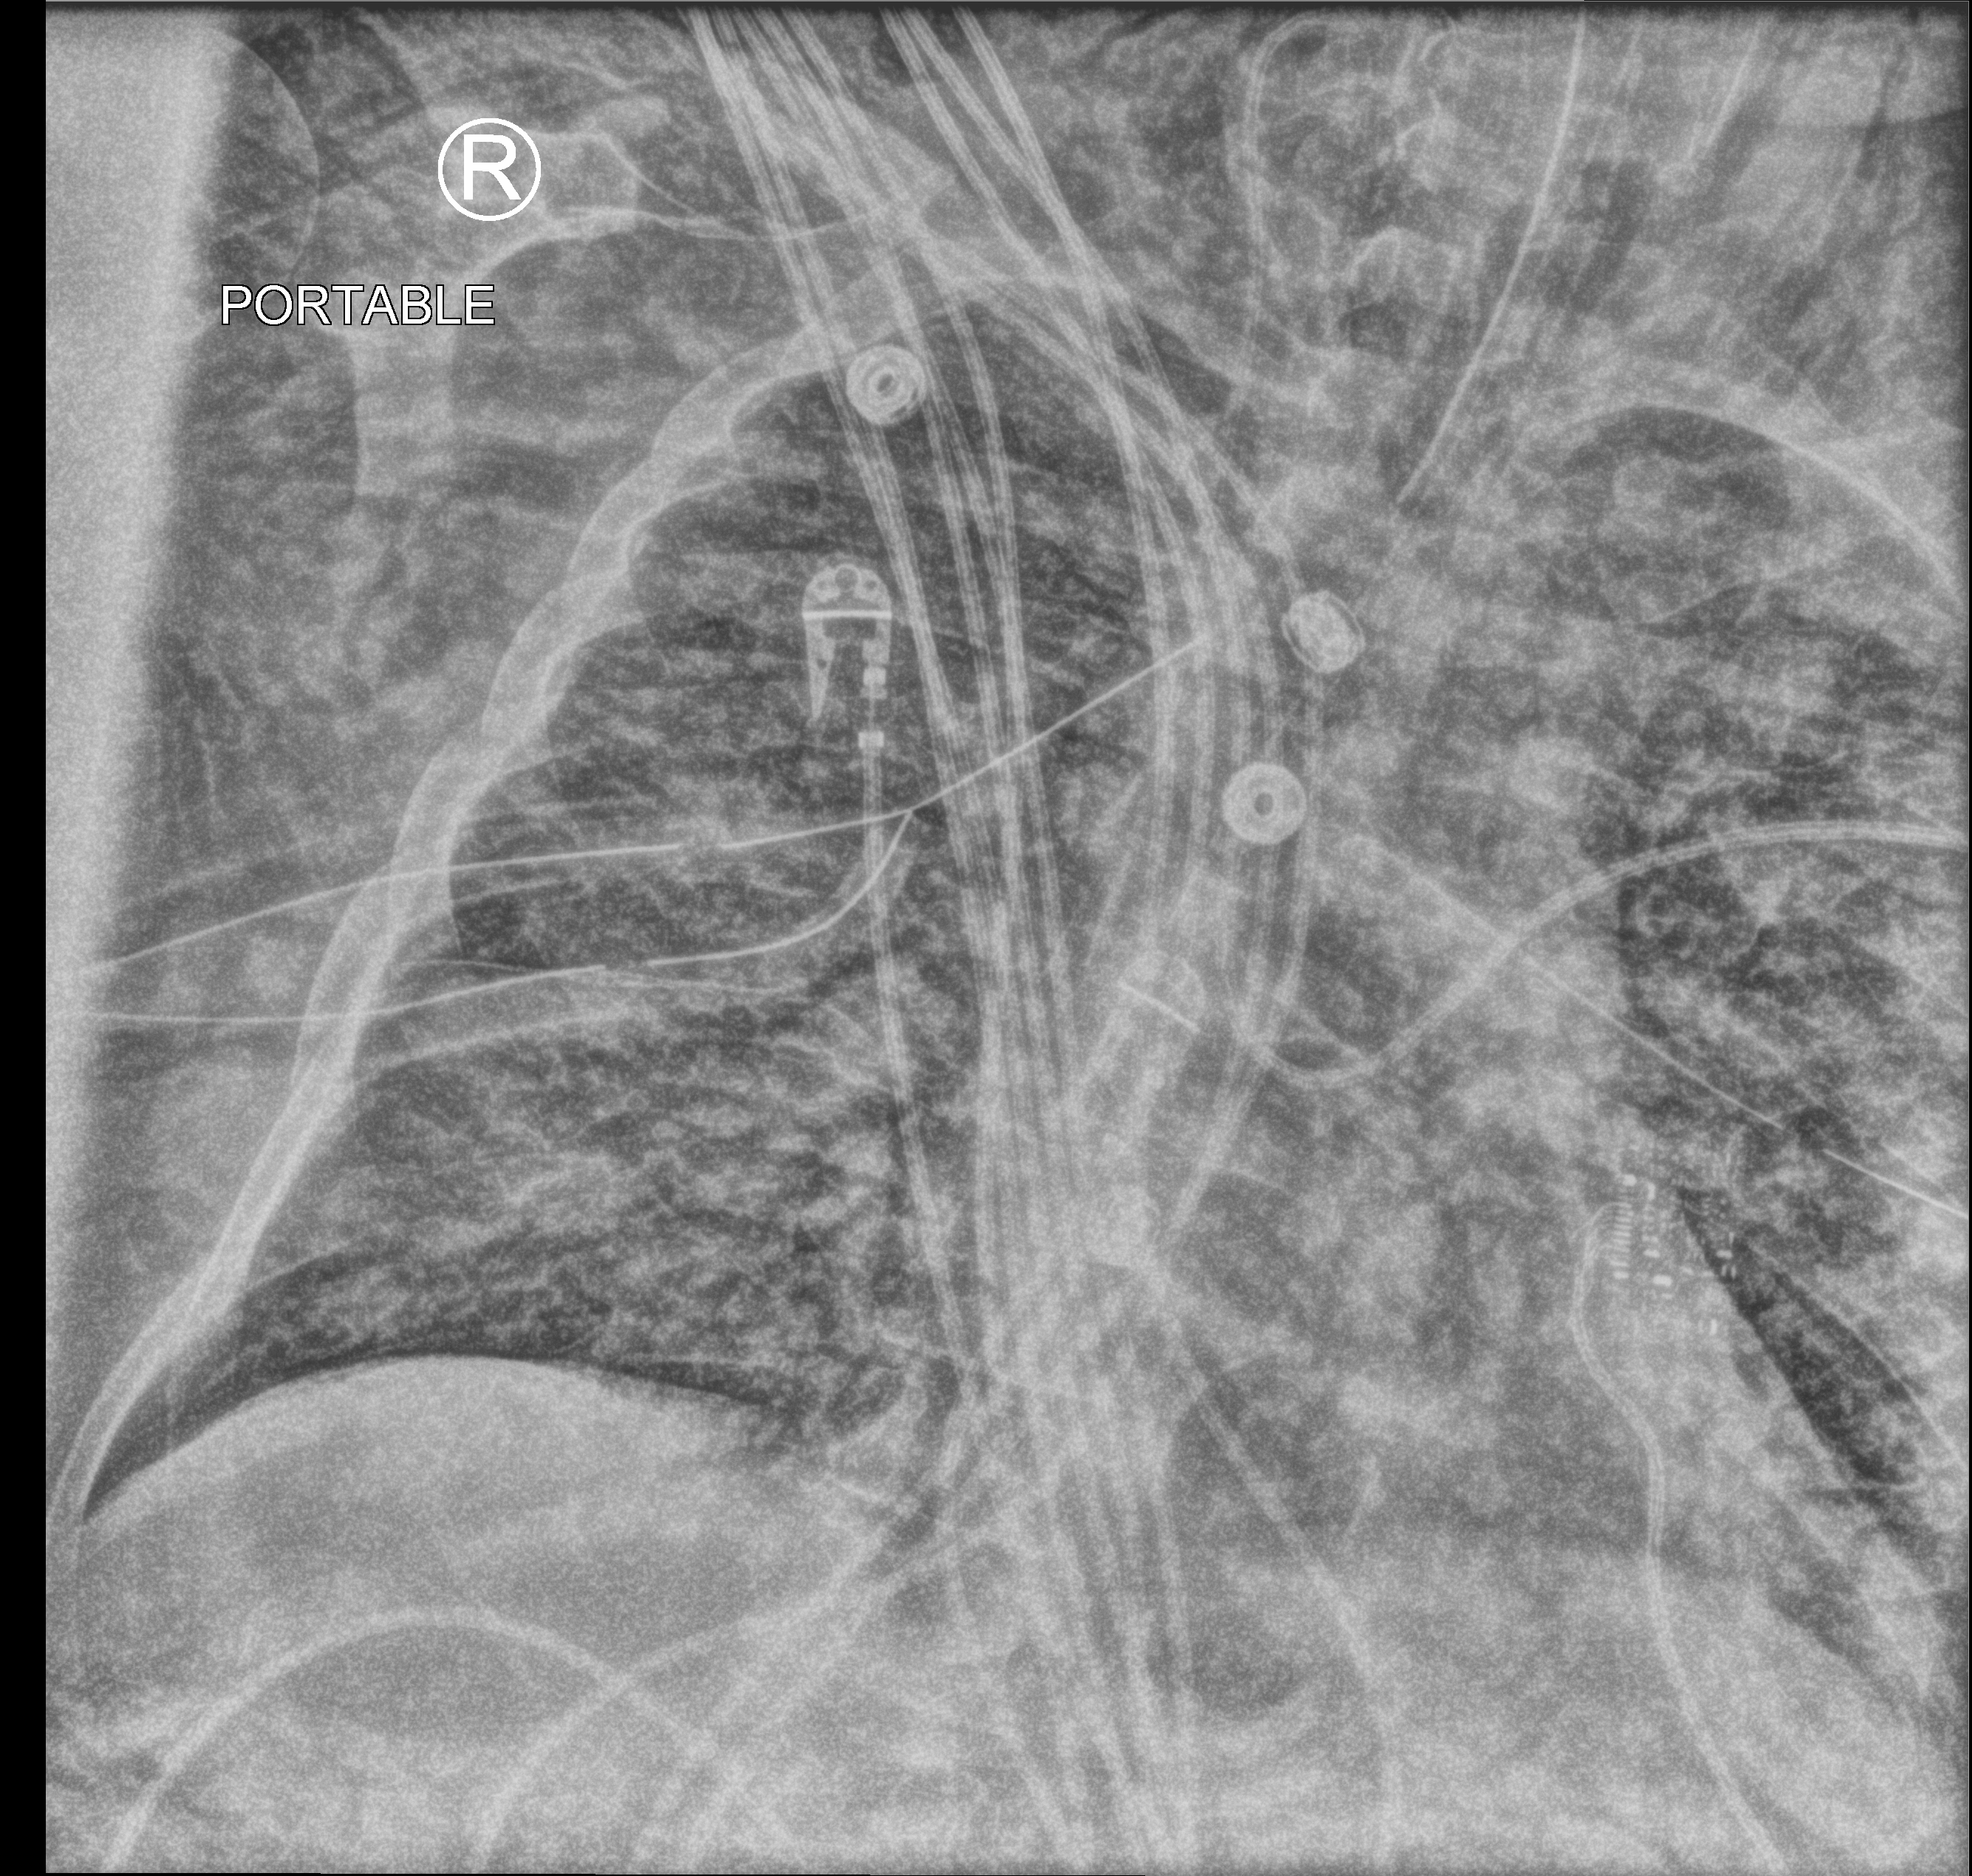
Portable chest radiograph, anteroposterior (AP) projection. Adult patient hospitalised with COVID-19, age 18–59 years.
Admission-level facts for this patient (not findings on this image; timing relative to this image not recorded): hypertension (admission record): yes; smoking status (admission record): never.